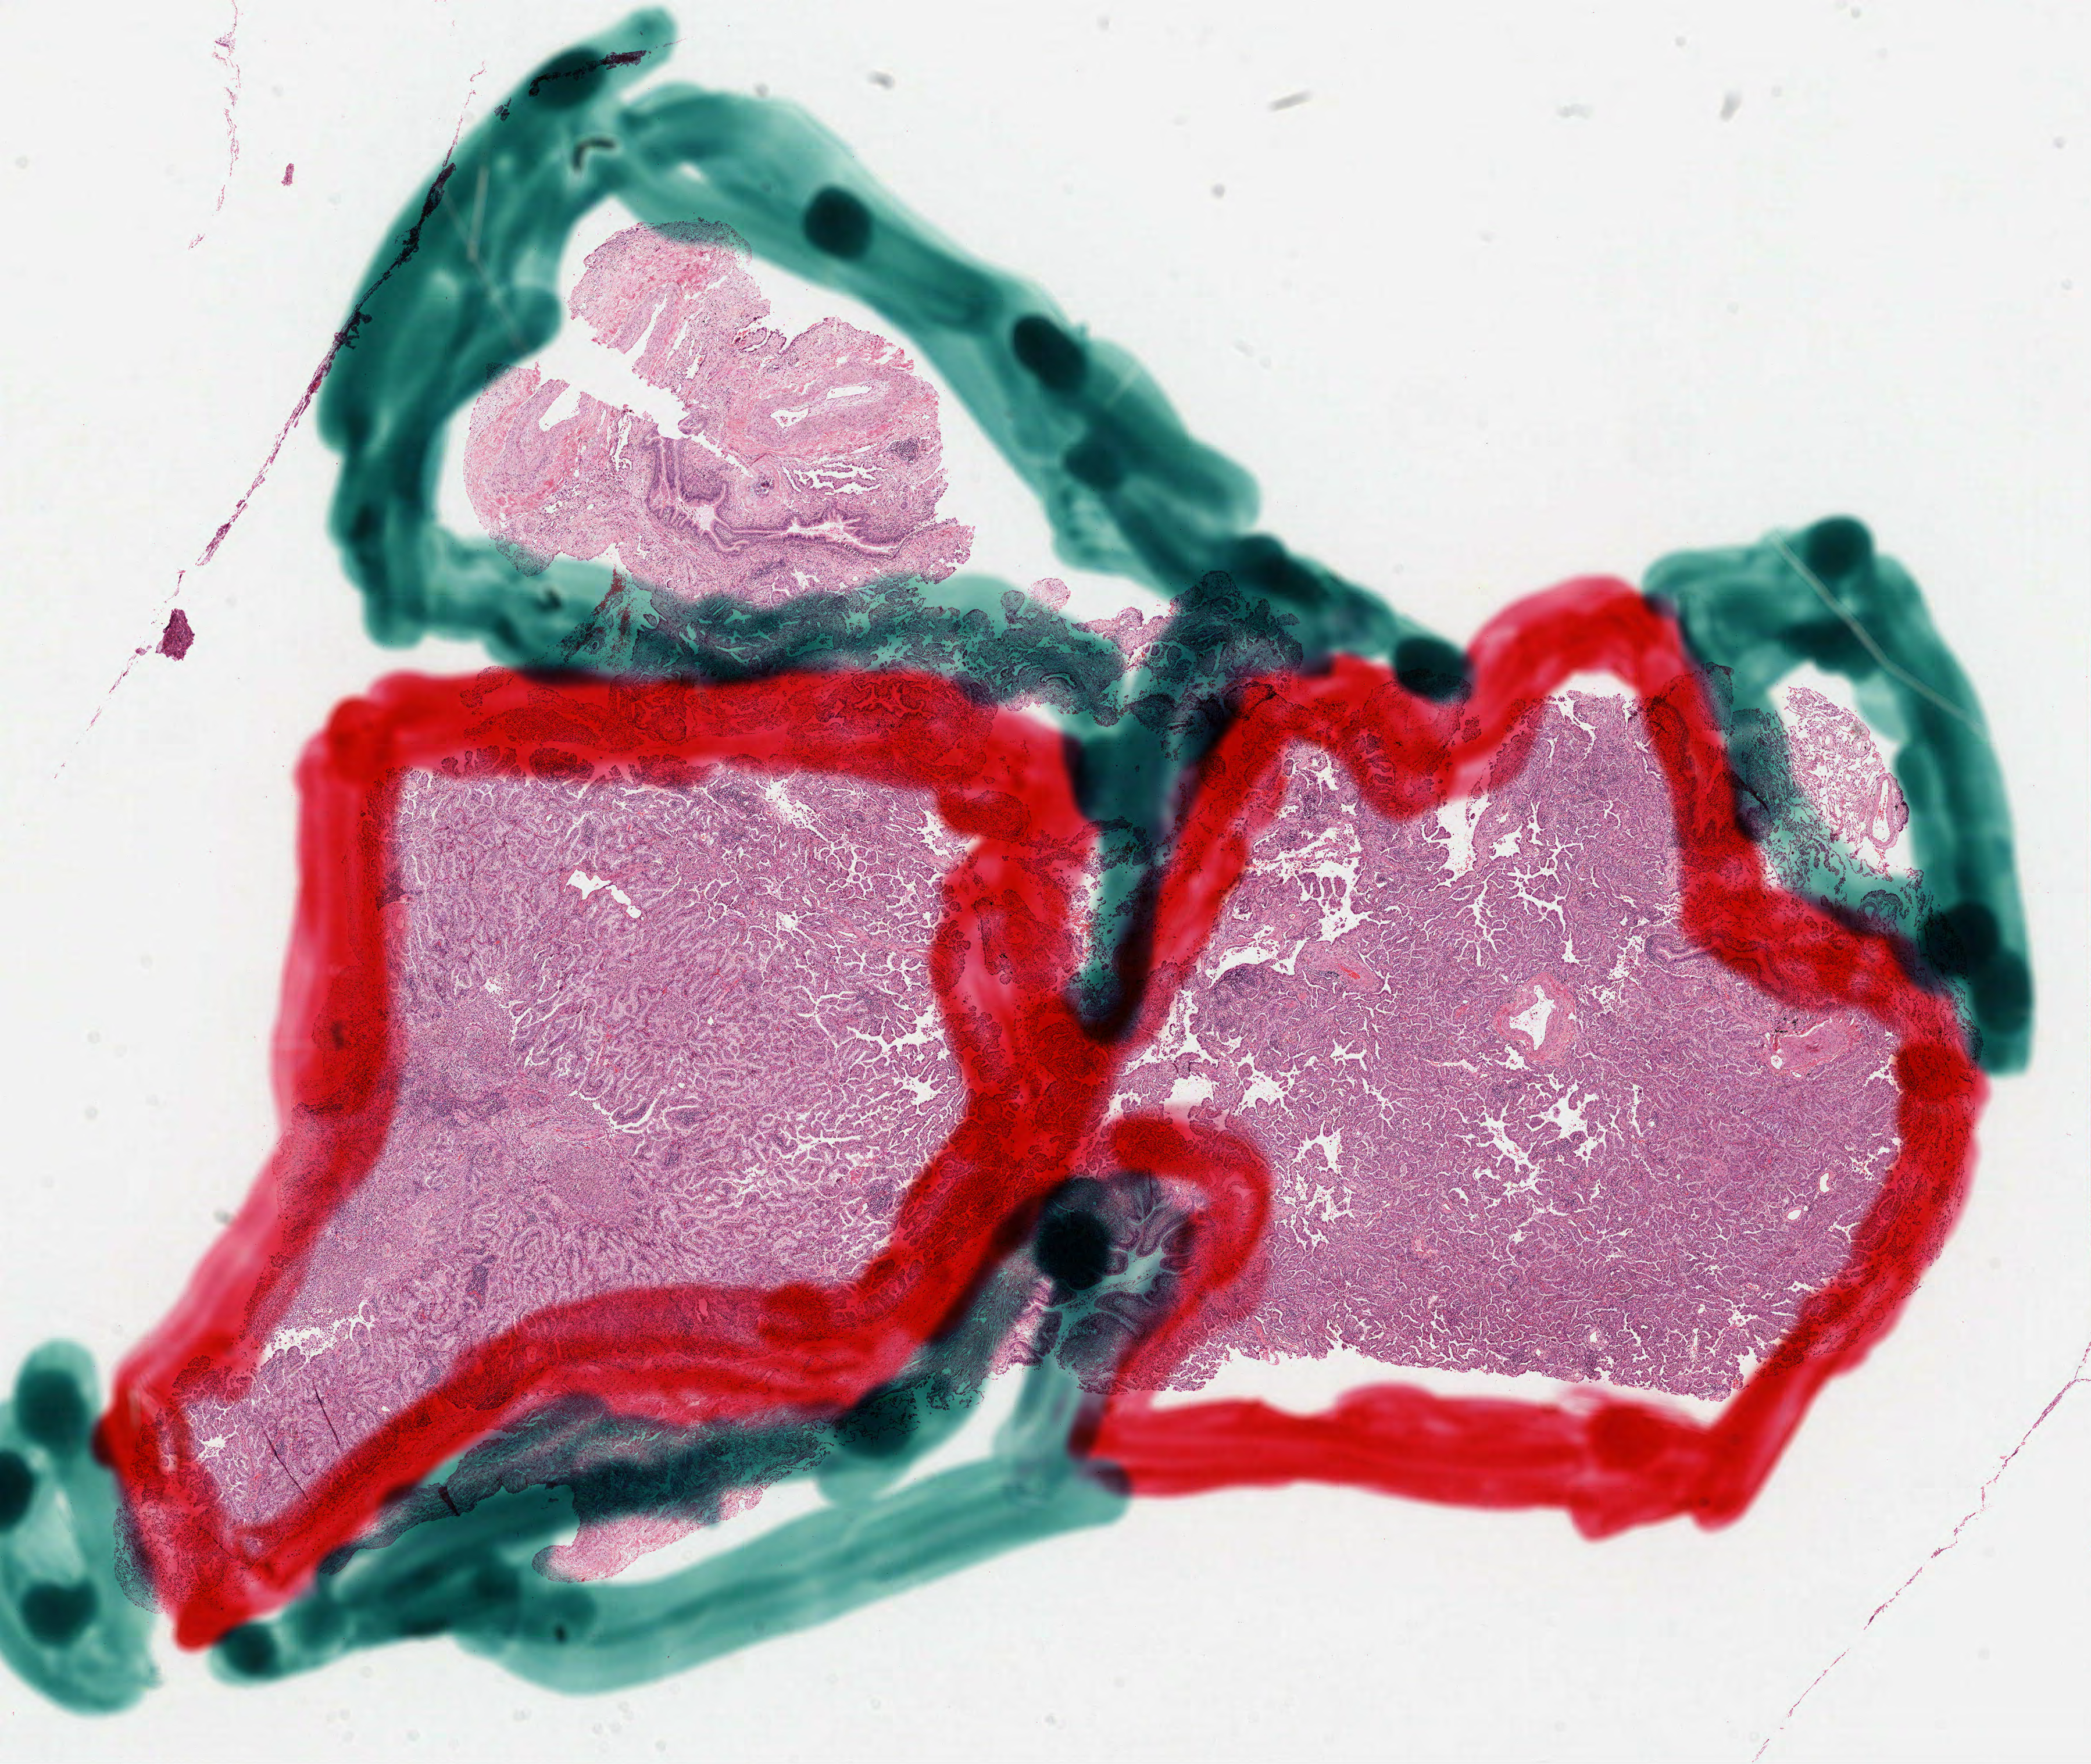
H&E-stained whole-slide image, low-resolution overview of the scanned area, about 14.5 x 12.2 mm (acquisition: 40x scan), formalin-fixed paraffin-embedded (FFPE) diagnostic section, sample: primary tumour, lung. Female patient; age at initial diagnosis 63 years.
Histologic diagnosis: Adenocarcinoma with mixed subtypes (upper lobe, lung). AJCC pathologic stage: IIIA (7th edition).